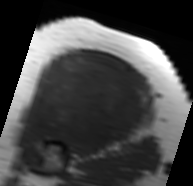
MRI of an extremity soft-tissue mass, one axial slice; slice 47 of 91 in the series (ordered by position); MR volume resampled by the dataset authors to the PET/CT grid (not the native acquisition matrix); 193 × 186 image matrix, field of view 188 × 182 mm. Female patient. From the clinical record (not read from this slice): histological type: malignant solitary fibrous tumor; grade: intermediate; site of the primary tumour: right thigh.
Structures marked on this image (expert contour drawn on MRI and transferred to this co-registered scan by the dataset authors):
- gross tumour volume including surrounding oedema: bounding box [x1, y1, x2, y2] px = [21, 53, 150, 152]
- gross tumour volume (mass): [26, 53, 146, 148]